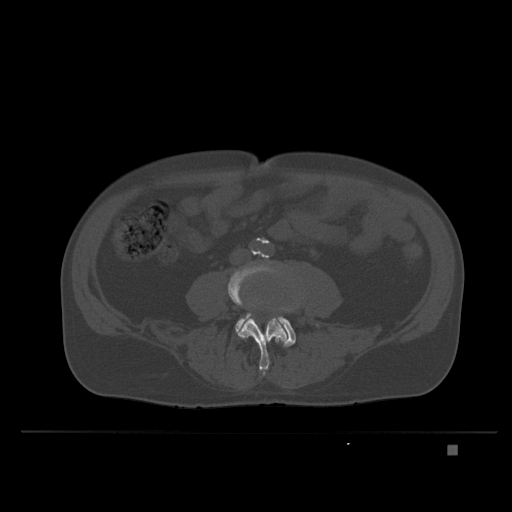
CT including the spine, one axial slice. Position 69 of 435 along the scan axis. Bone window (W 1800 / L 400 HU). 1.5 mm slice thickness. 512 × 512 image matrix. Male patient, age 73 years. Case-level facts recorded for this patient, not image findings: primary cancer: skin.
Annotated regions visible in this slice (semi-automatically segmented with operator editing):
- L4 vertebra: bounding box <228,262,295,376> (left, top, right, bottom; pixels)
- L5 vertebra: <235,294,304,347>